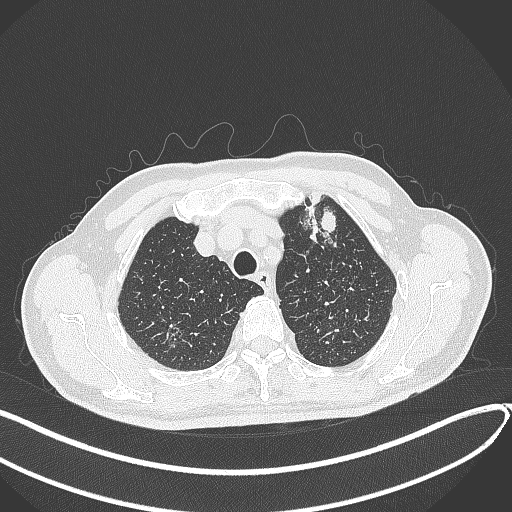
Chest CT, one axial slice. Slice 351 of 459 in the series (ordered by position). Reconstruction kernel B70f. 120 kVp. Lung window (W 1500 / L -600 HU). 1 mm slice thickness. 512 × 512 image matrix, field of view 400 × 400 mm. Male patient, age 74 years. From the clinical record (not read from this slice): clinical TNM (as recorded): T2b N0 M1c.
Outlined on this slice (bounding box drawn by a radiologist):
- lung tumour (recorded histology: adenocarcinoma): bounding box [x1, y1, x2, y2] px = [302, 193, 343, 248]